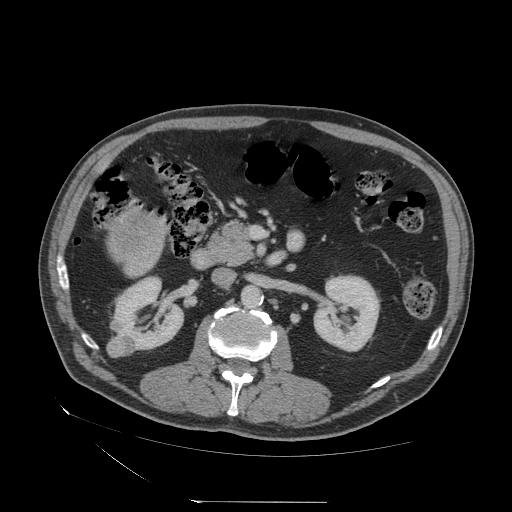
Contrast-enhanced abdominal CT (liver protocol), one axial slice; slice 6 of 83 in the series (ordered by position); reconstruction kernel STANDARD; soft-tissue window (W 400 / L 40 HU); 2.5 mm slice thickness; 512 × 512 image matrix, field of view 460 × 460 mm. Case-level facts recorded for this patient, not image findings: diagnosis: hepatocellular carcinoma (patient treated with transarterial chemoembolisation; whether this scan precedes or follows treatment is not stated here); TNM stage (as recorded): Stage-I.
Annotated regions visible in this slice (semi-automatic segmentation, software-assisted and operator-edited):
- mass: bounding box [x1, y1, x2, y2] px = [106, 210, 168, 260]